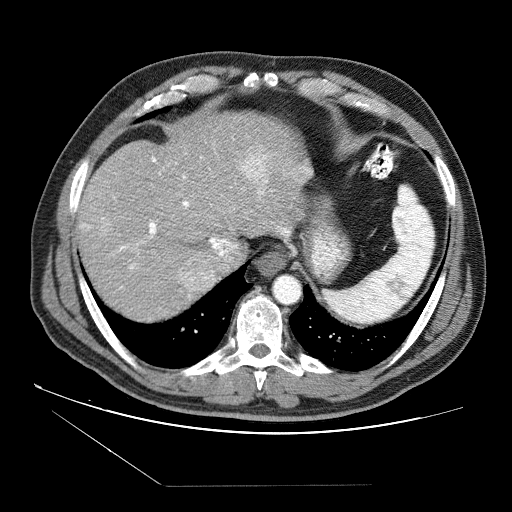
Contrast-enhanced abdominal CT (liver protocol), one axial slice; position 67 of 87 along the scan axis; reconstruction kernel STANDARD; 120 kVp; soft-tissue window (W 400 / L 40 HU); 512 × 512 image matrix. From the clinical record (not read from this slice): diagnosis: hepatocellular carcinoma (patient treated with transarterial chemoembolisation; whether this scan precedes or follows treatment is not stated here); TNM stage (as recorded): Stage-II; Child-Pugh class: B; tumour nodularity: multinodular.
Structures marked on this image (semi-automatic segmentation, software-assisted and operator-edited):
- abdominal aorta: bounding box (x1, y1, x2, y2) in pixels: (273, 276, 300, 303)
- liver parenchyma outside the tumour (the mass and vessels are separate outlines, so this box may not span the whole liver): (78, 112, 312, 320)
- mass: (99, 146, 269, 298)
- liver vessels: (80, 137, 310, 288)